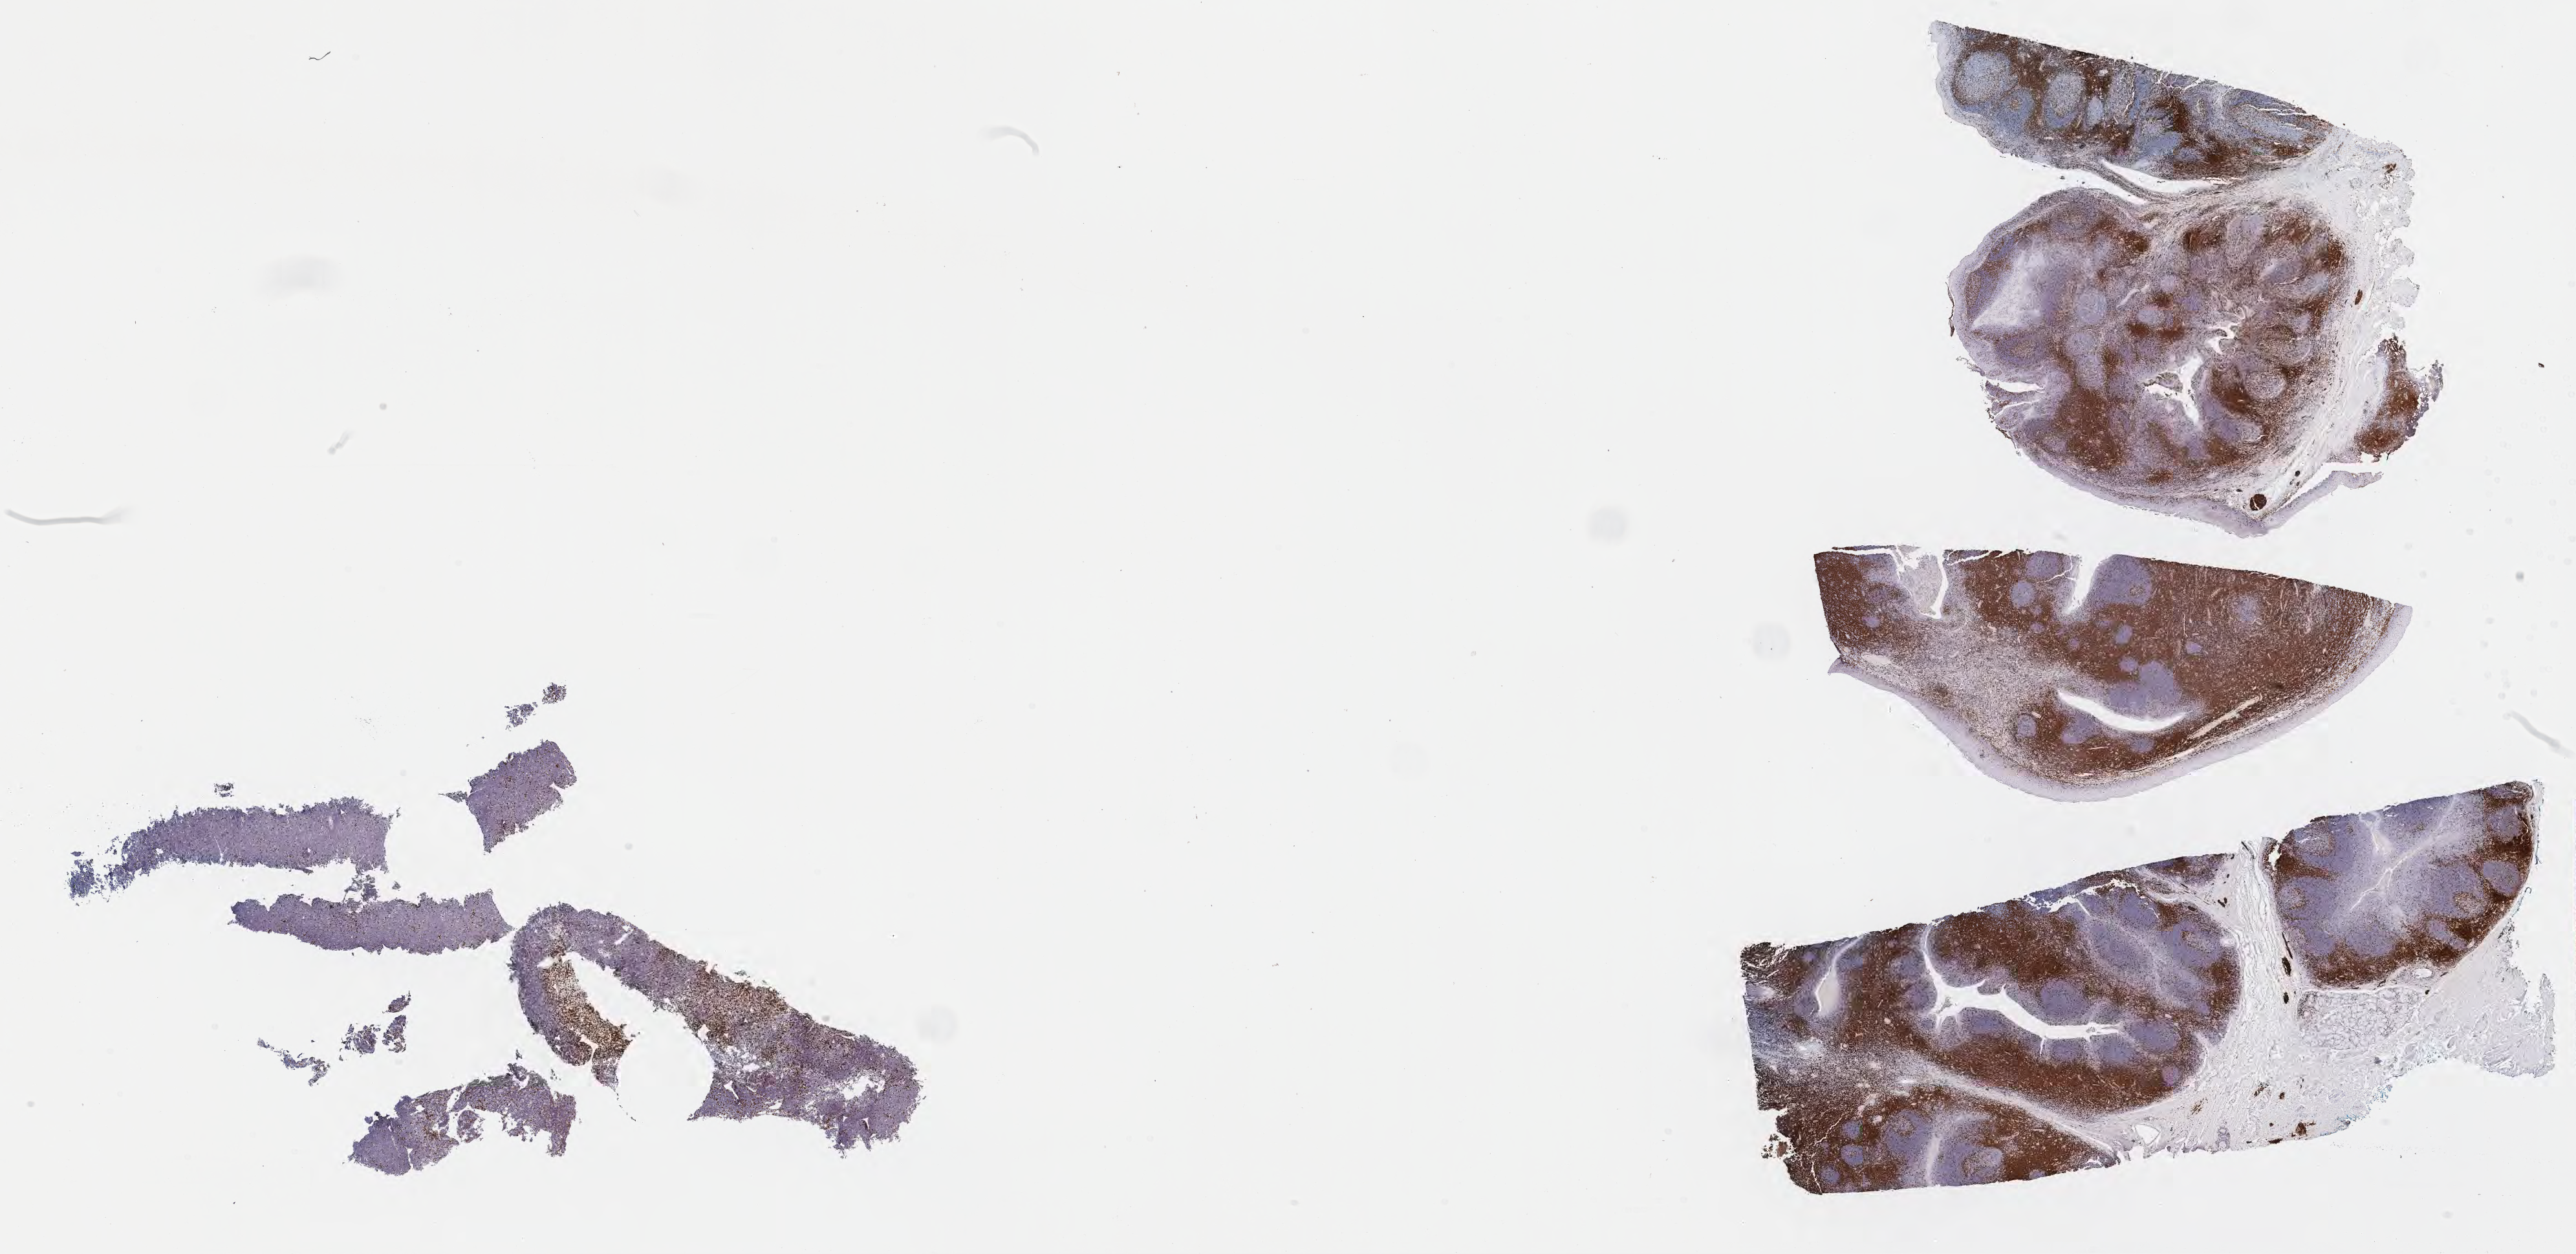
IHC for CD3, whole-slide image, whole scanned area (about 32.2 x 15.7 mm) shown as a low-resolution overview, specimen: tumor tissue, site: liver. Male patient; age at initial diagnosis 4 years.
Diagnosis: Burkitt lymphoma, NOS.